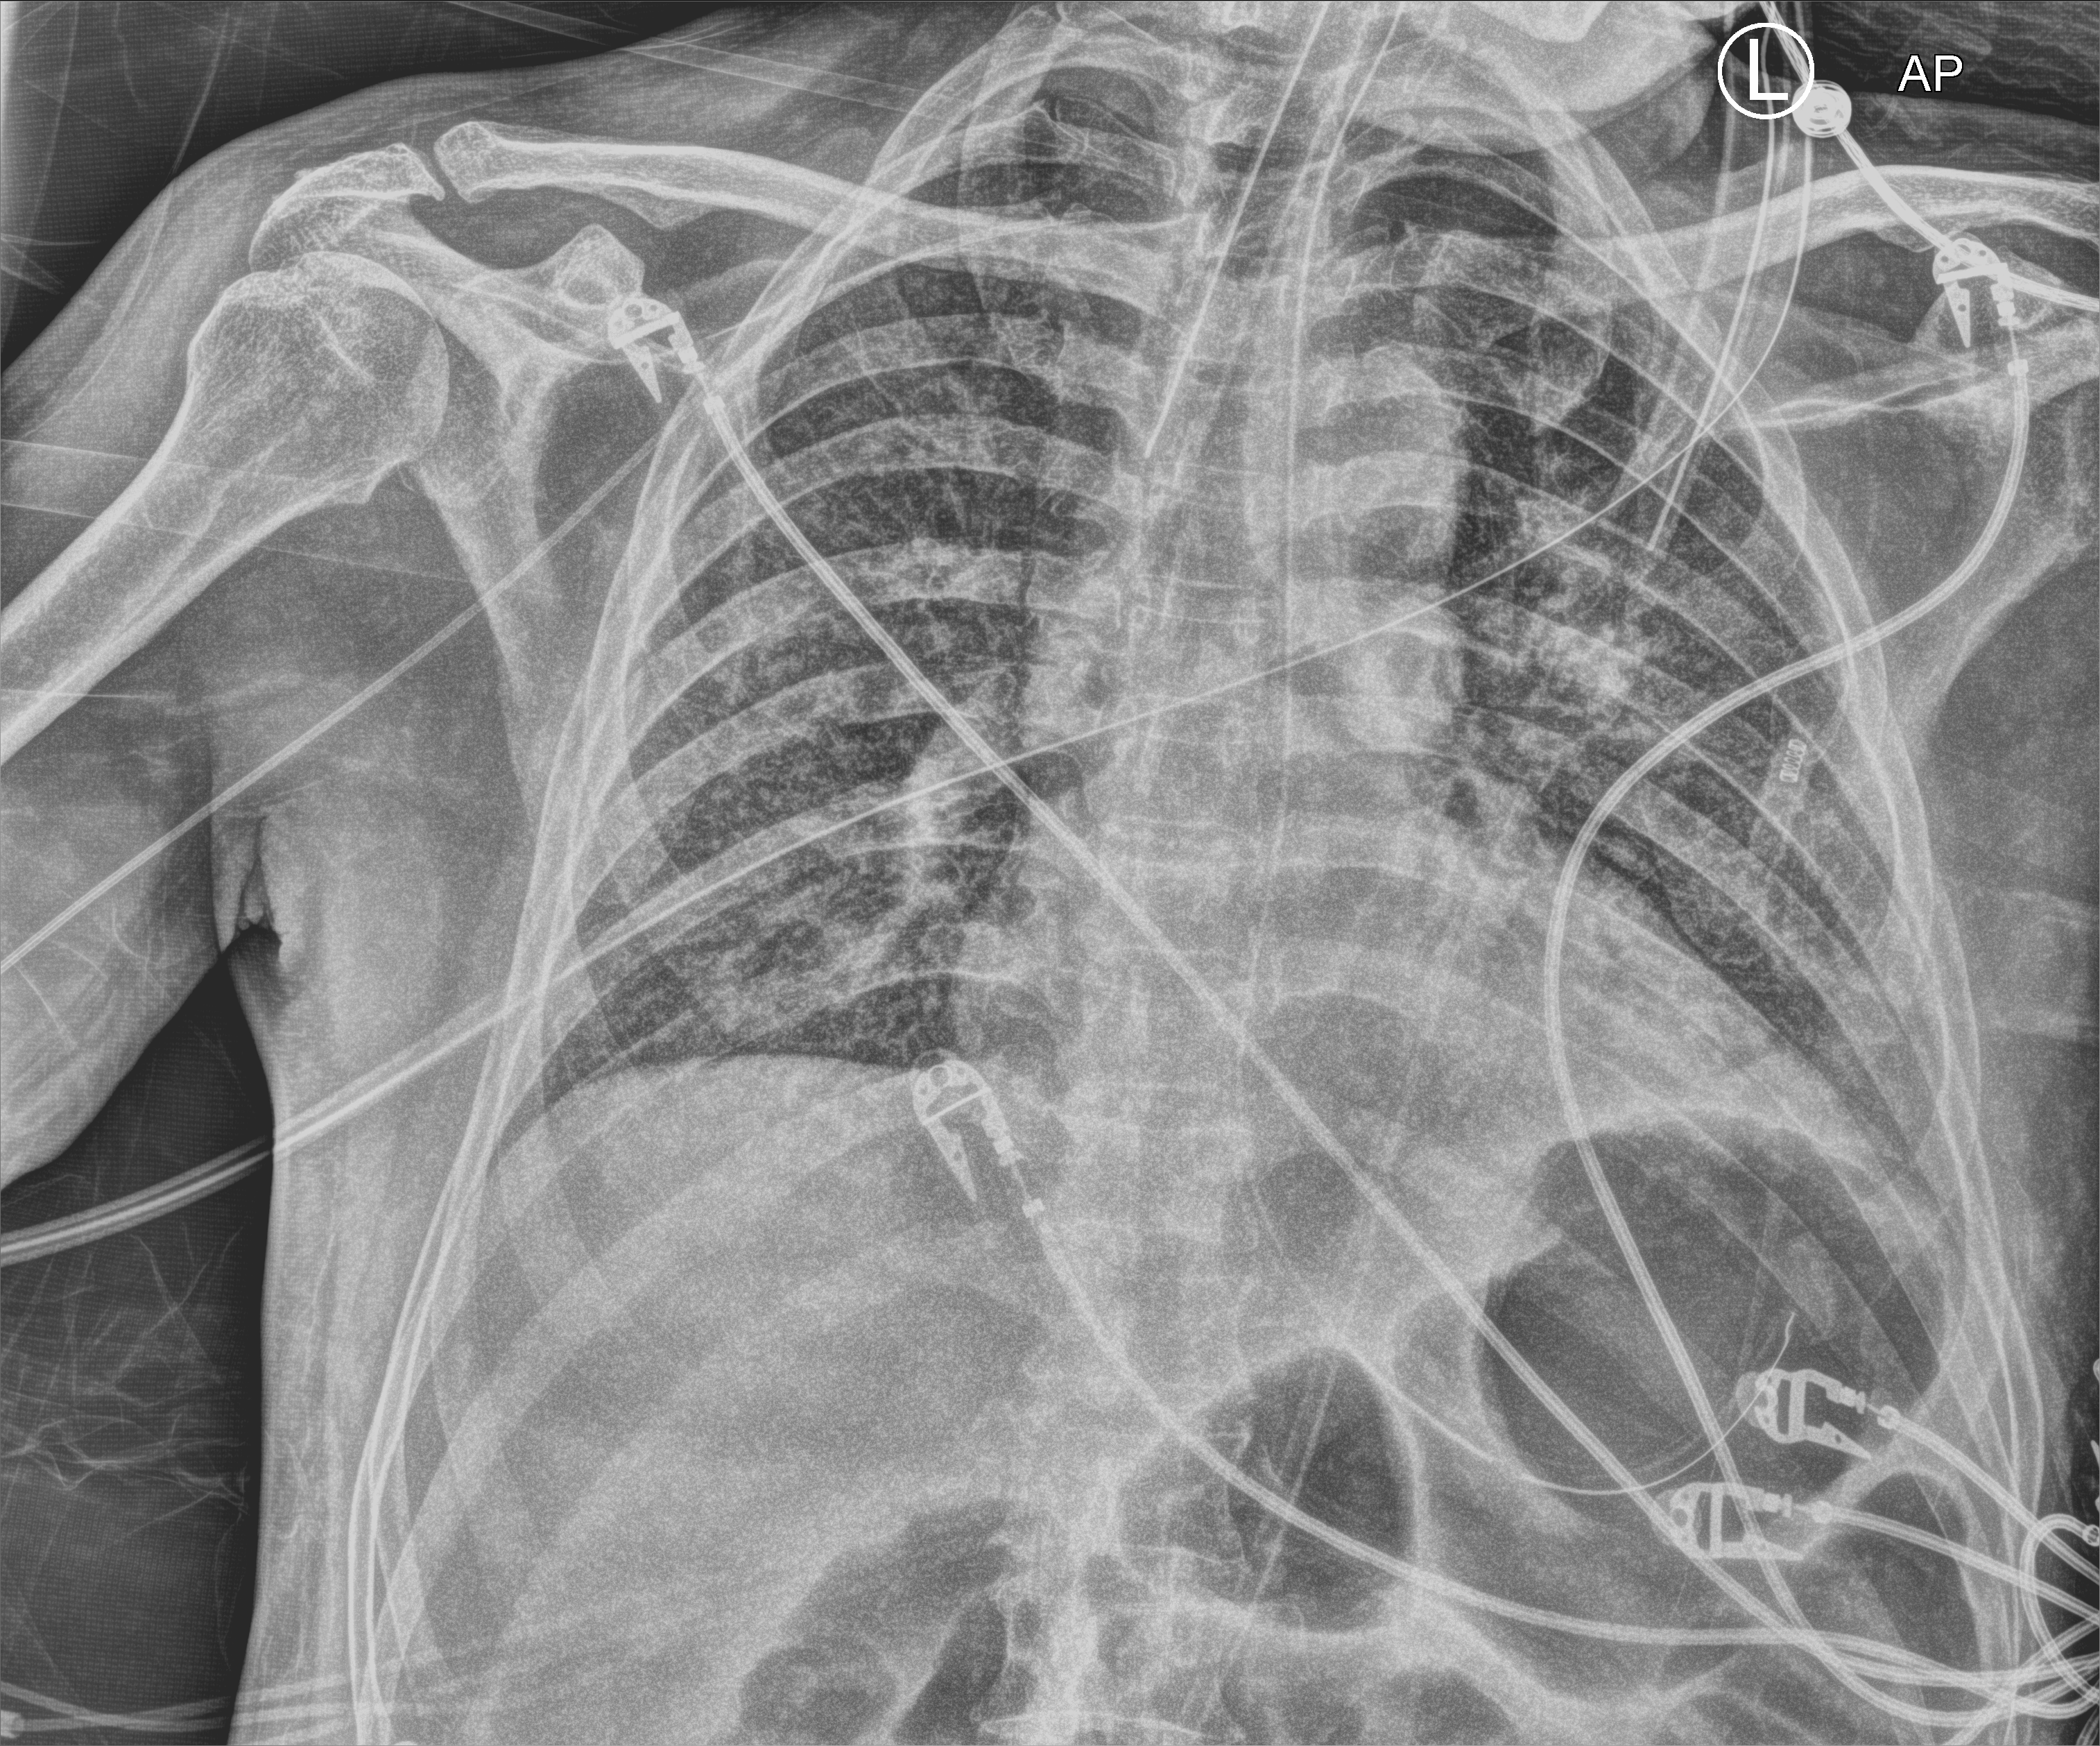
Bedside chest radiograph (computed radiography); anteroposterior (AP) projection. Male patient hospitalised with COVID-19, age 60–74 years.
From the hospital-stay record, not from the radiograph (when in the stay this image was taken is not recorded):
- length of hospital stay: 37 days
- mechanically ventilated during this hospital stay: yes
- COPD (admission record): no